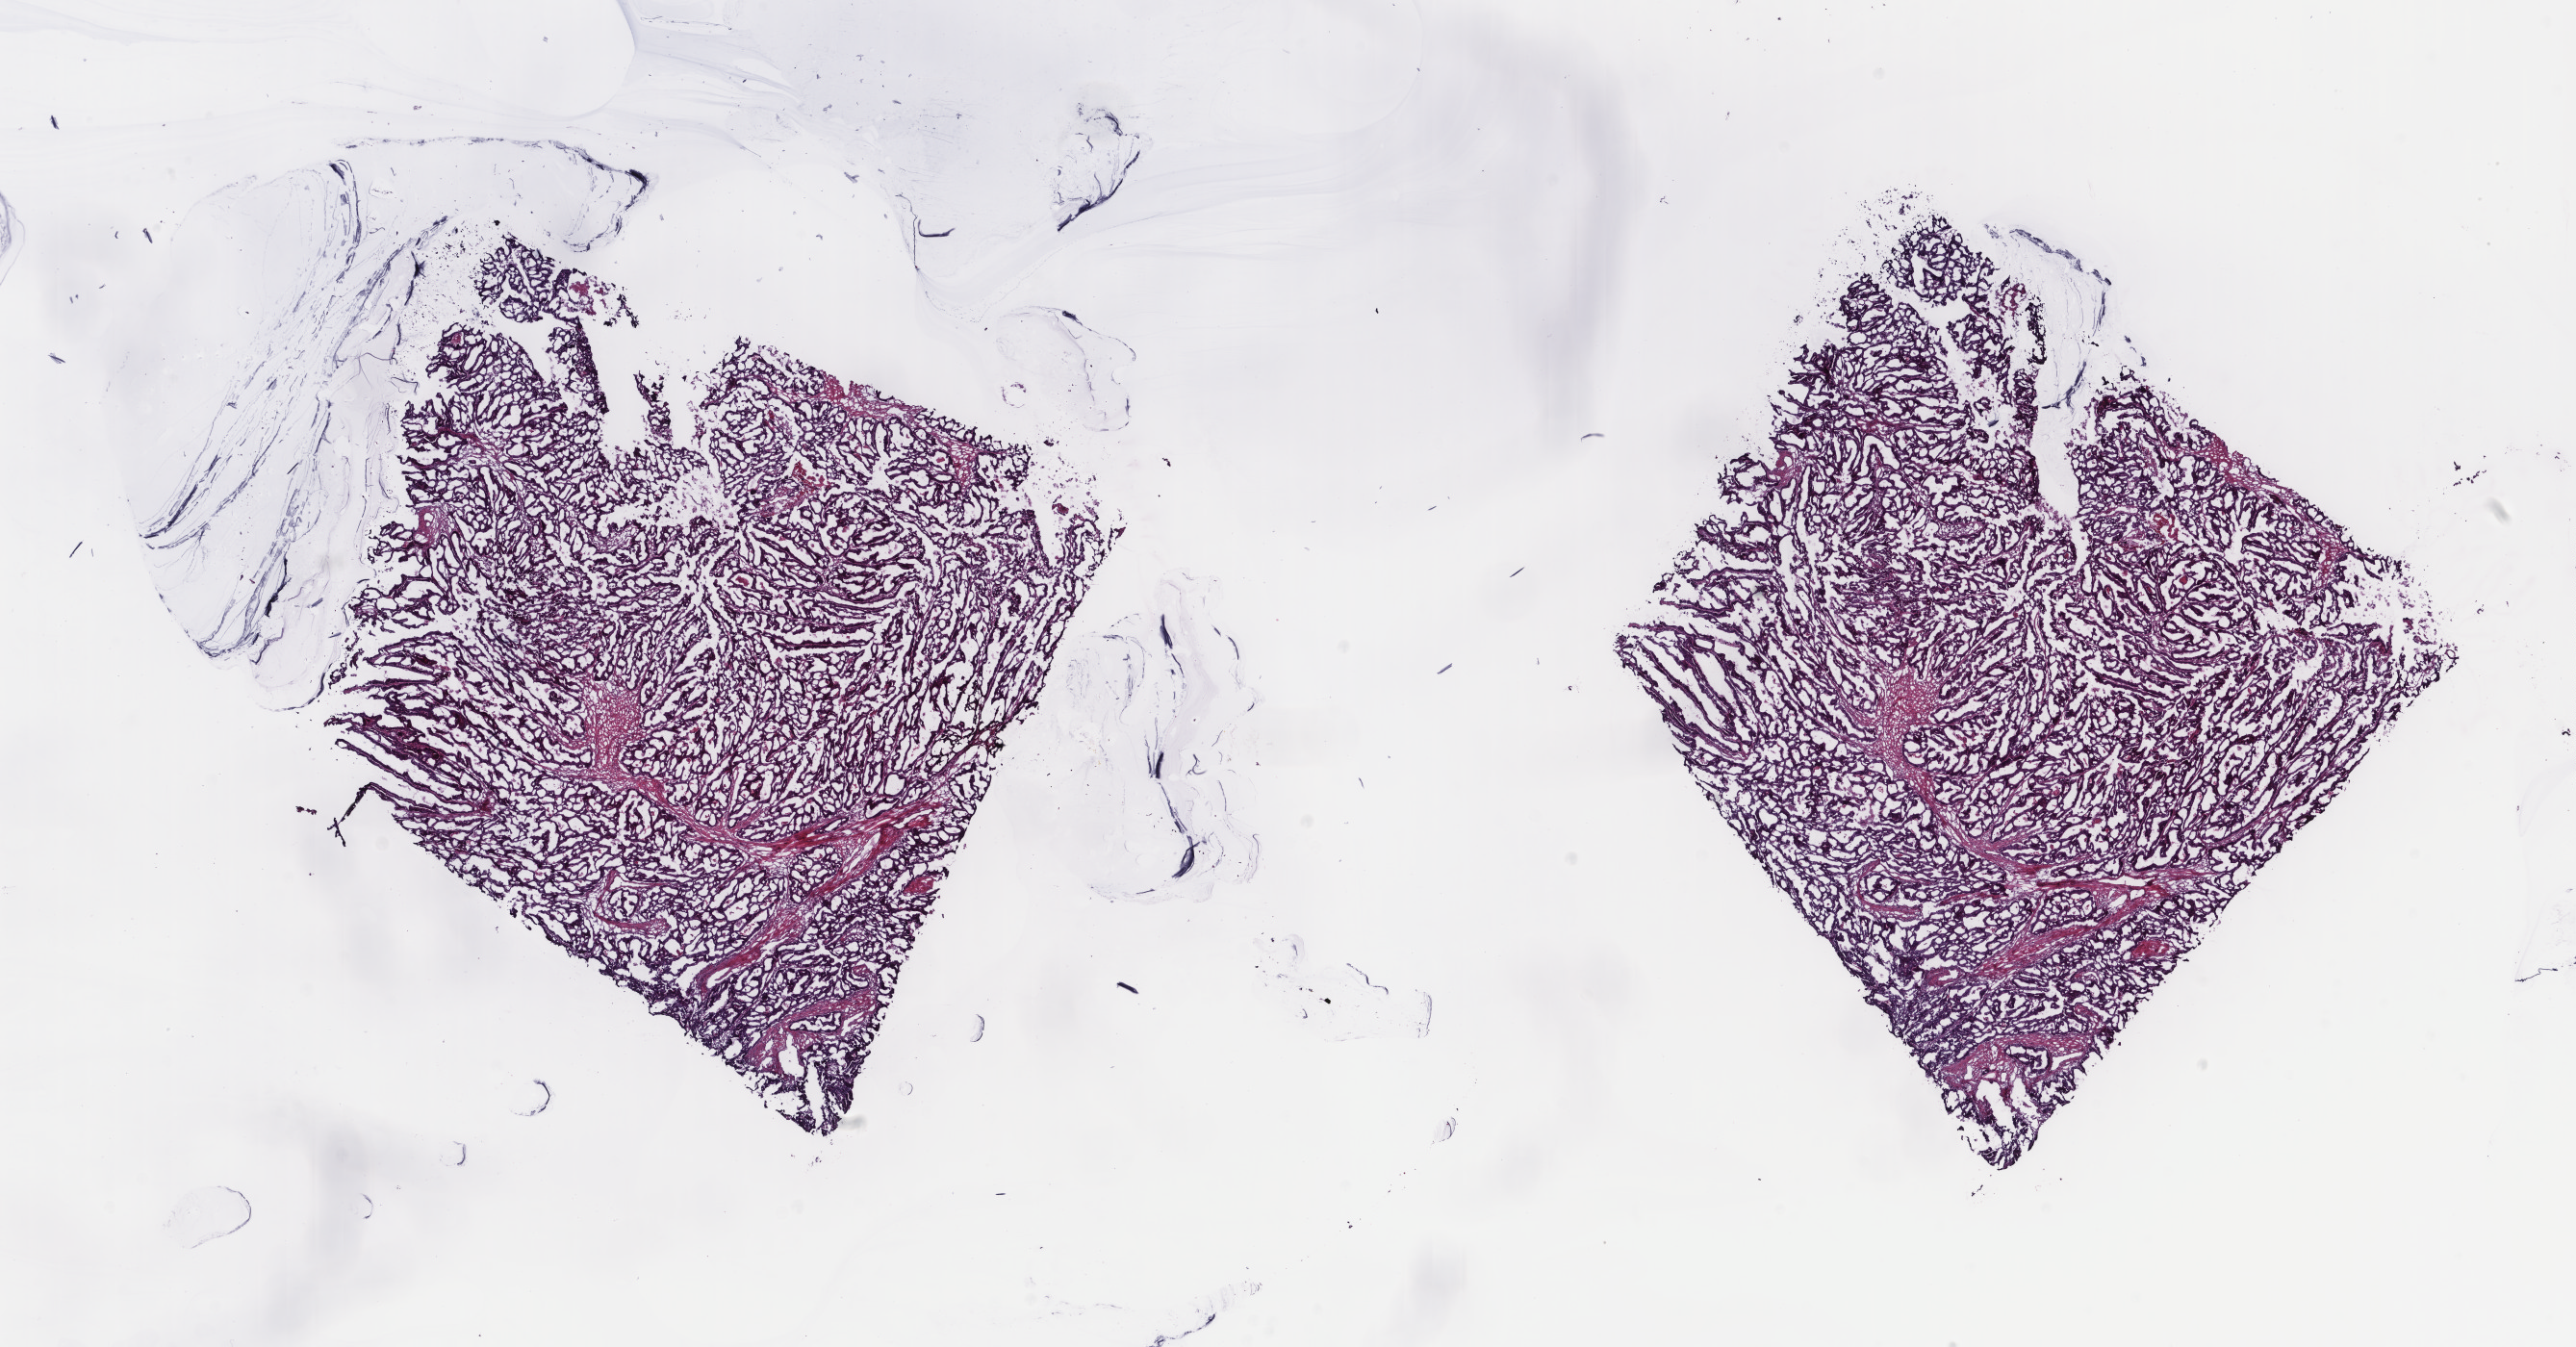
Digitized H&E tissue section (whole slide) — a low-resolution overview of the entire scanned area, about 21.2 x 11.1 mm (slide scanned at 40x), frozen section from the top of the tissue portion, primary tumour sample from the rectum. Male patient; age at initial diagnosis 75 years. Composition of this section per pathologist review: tumour cells 100%, tumour nuclei 95%, normal cells 0%, stromal cells 0%, necrosis 0%. Inflammatory infiltration, as recorded: lymphocyte infiltration 0%, monocyte infiltration 0%, neutrophil infiltration 0%.
Lymph nodes positive (case pathology): 2 of 8 examined. Pathologic diagnosis: Adenocarcinoma, NOS. TNM: T3 N1 M1. AJCC pathologic stage: IVA.